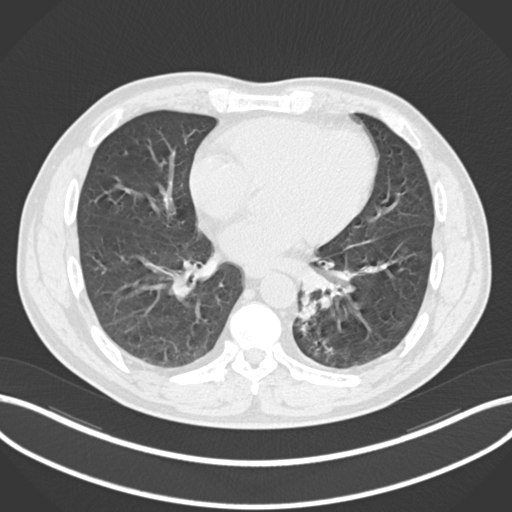
Chest CT, one axial slice. Position 85 of 223 along the scan axis. Lung window (W 1500 / L -600 HU). 1 mm slice thickness. 512 × 512 image matrix, field of view 400 × 400 mm. Patient: male, 50 years. Case-level facts recorded for this patient, not image findings: clinical TNM (as recorded): T2a N3 M0.
Structures marked on this image (rectangle marked by the reading radiologist):
- lung tumour (recorded histology: squamous cell carcinoma): bounding box <292,292,319,328> (left, top, right, bottom; pixels)